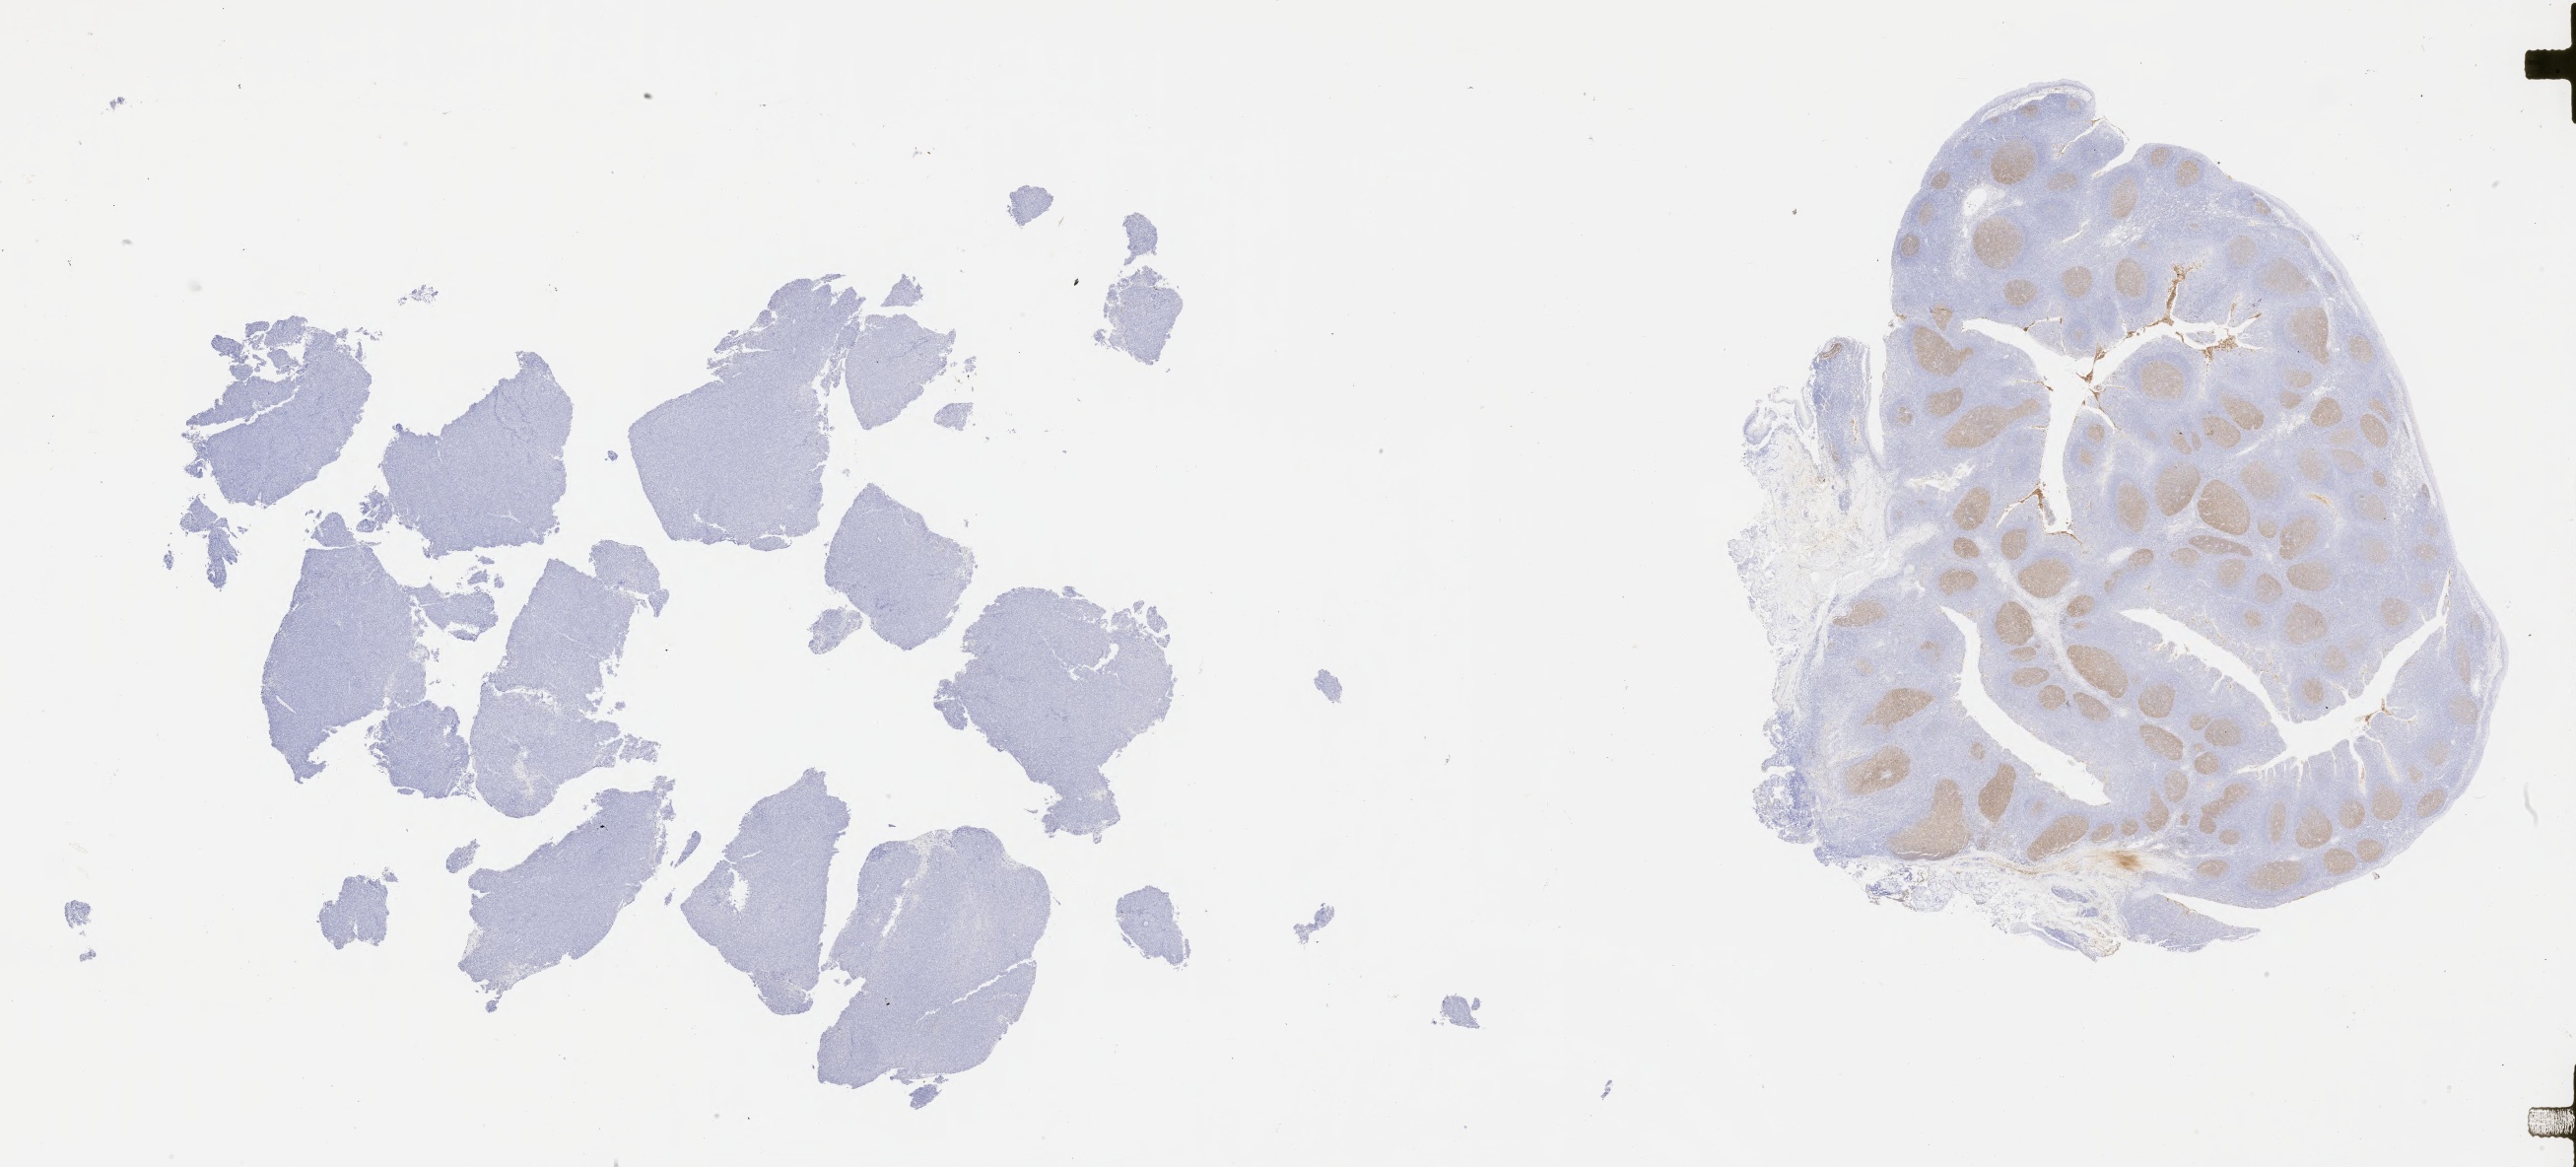
Whole-slide image, immunohistochemical stain for CD10 — whole scanned area (about 42.3 x 19.1 mm) shown as a low-resolution overview. Tumor tissue. Site: lymph node. Female patient, 50 years old.
Diagnosis: Diffuse large B-cell lymphoma, NOS.